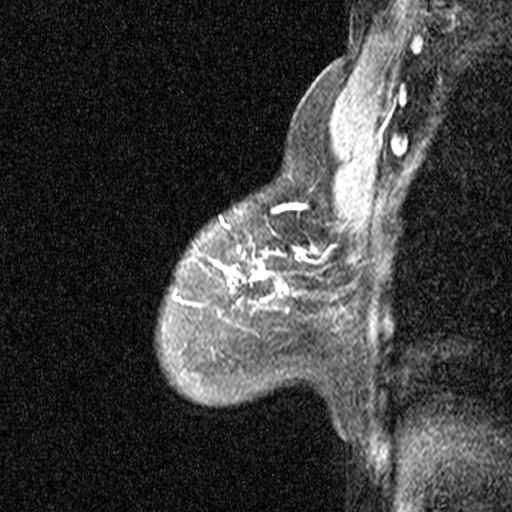
Breast MRI (dynamic contrast-enhanced), one sagittal slice; dynamic contrast-enhanced study with each time point stored as its own series, time point 2 of 3 at this slice position (early post-contrast, ordered by acquisition time); 1.5 T; TE 4.5 ms, TR 11 ms; 3 mm slice thickness; 512 × 512 image matrix, field of view 200 × 200 mm. Patient: female, 53 years. Case-level facts recorded for this patient, not image findings: setting: breast cancer imaged before/during neoadjuvant chemotherapy; receptor status: HR-positive, HER2-negative.
Outlined on this slice (semi-automatically segmented with operator editing):
- analysis volume of interest (the breast-tissue region the enhancement analysis was run in; not a lesion): box from (x=88, y=176) to (x=313, y=423) px
- tumour enhancement mask (voxels above the 90 % enhancement threshold inside the analysis volume of interest): (x=225, y=204)–(x=308, y=292)